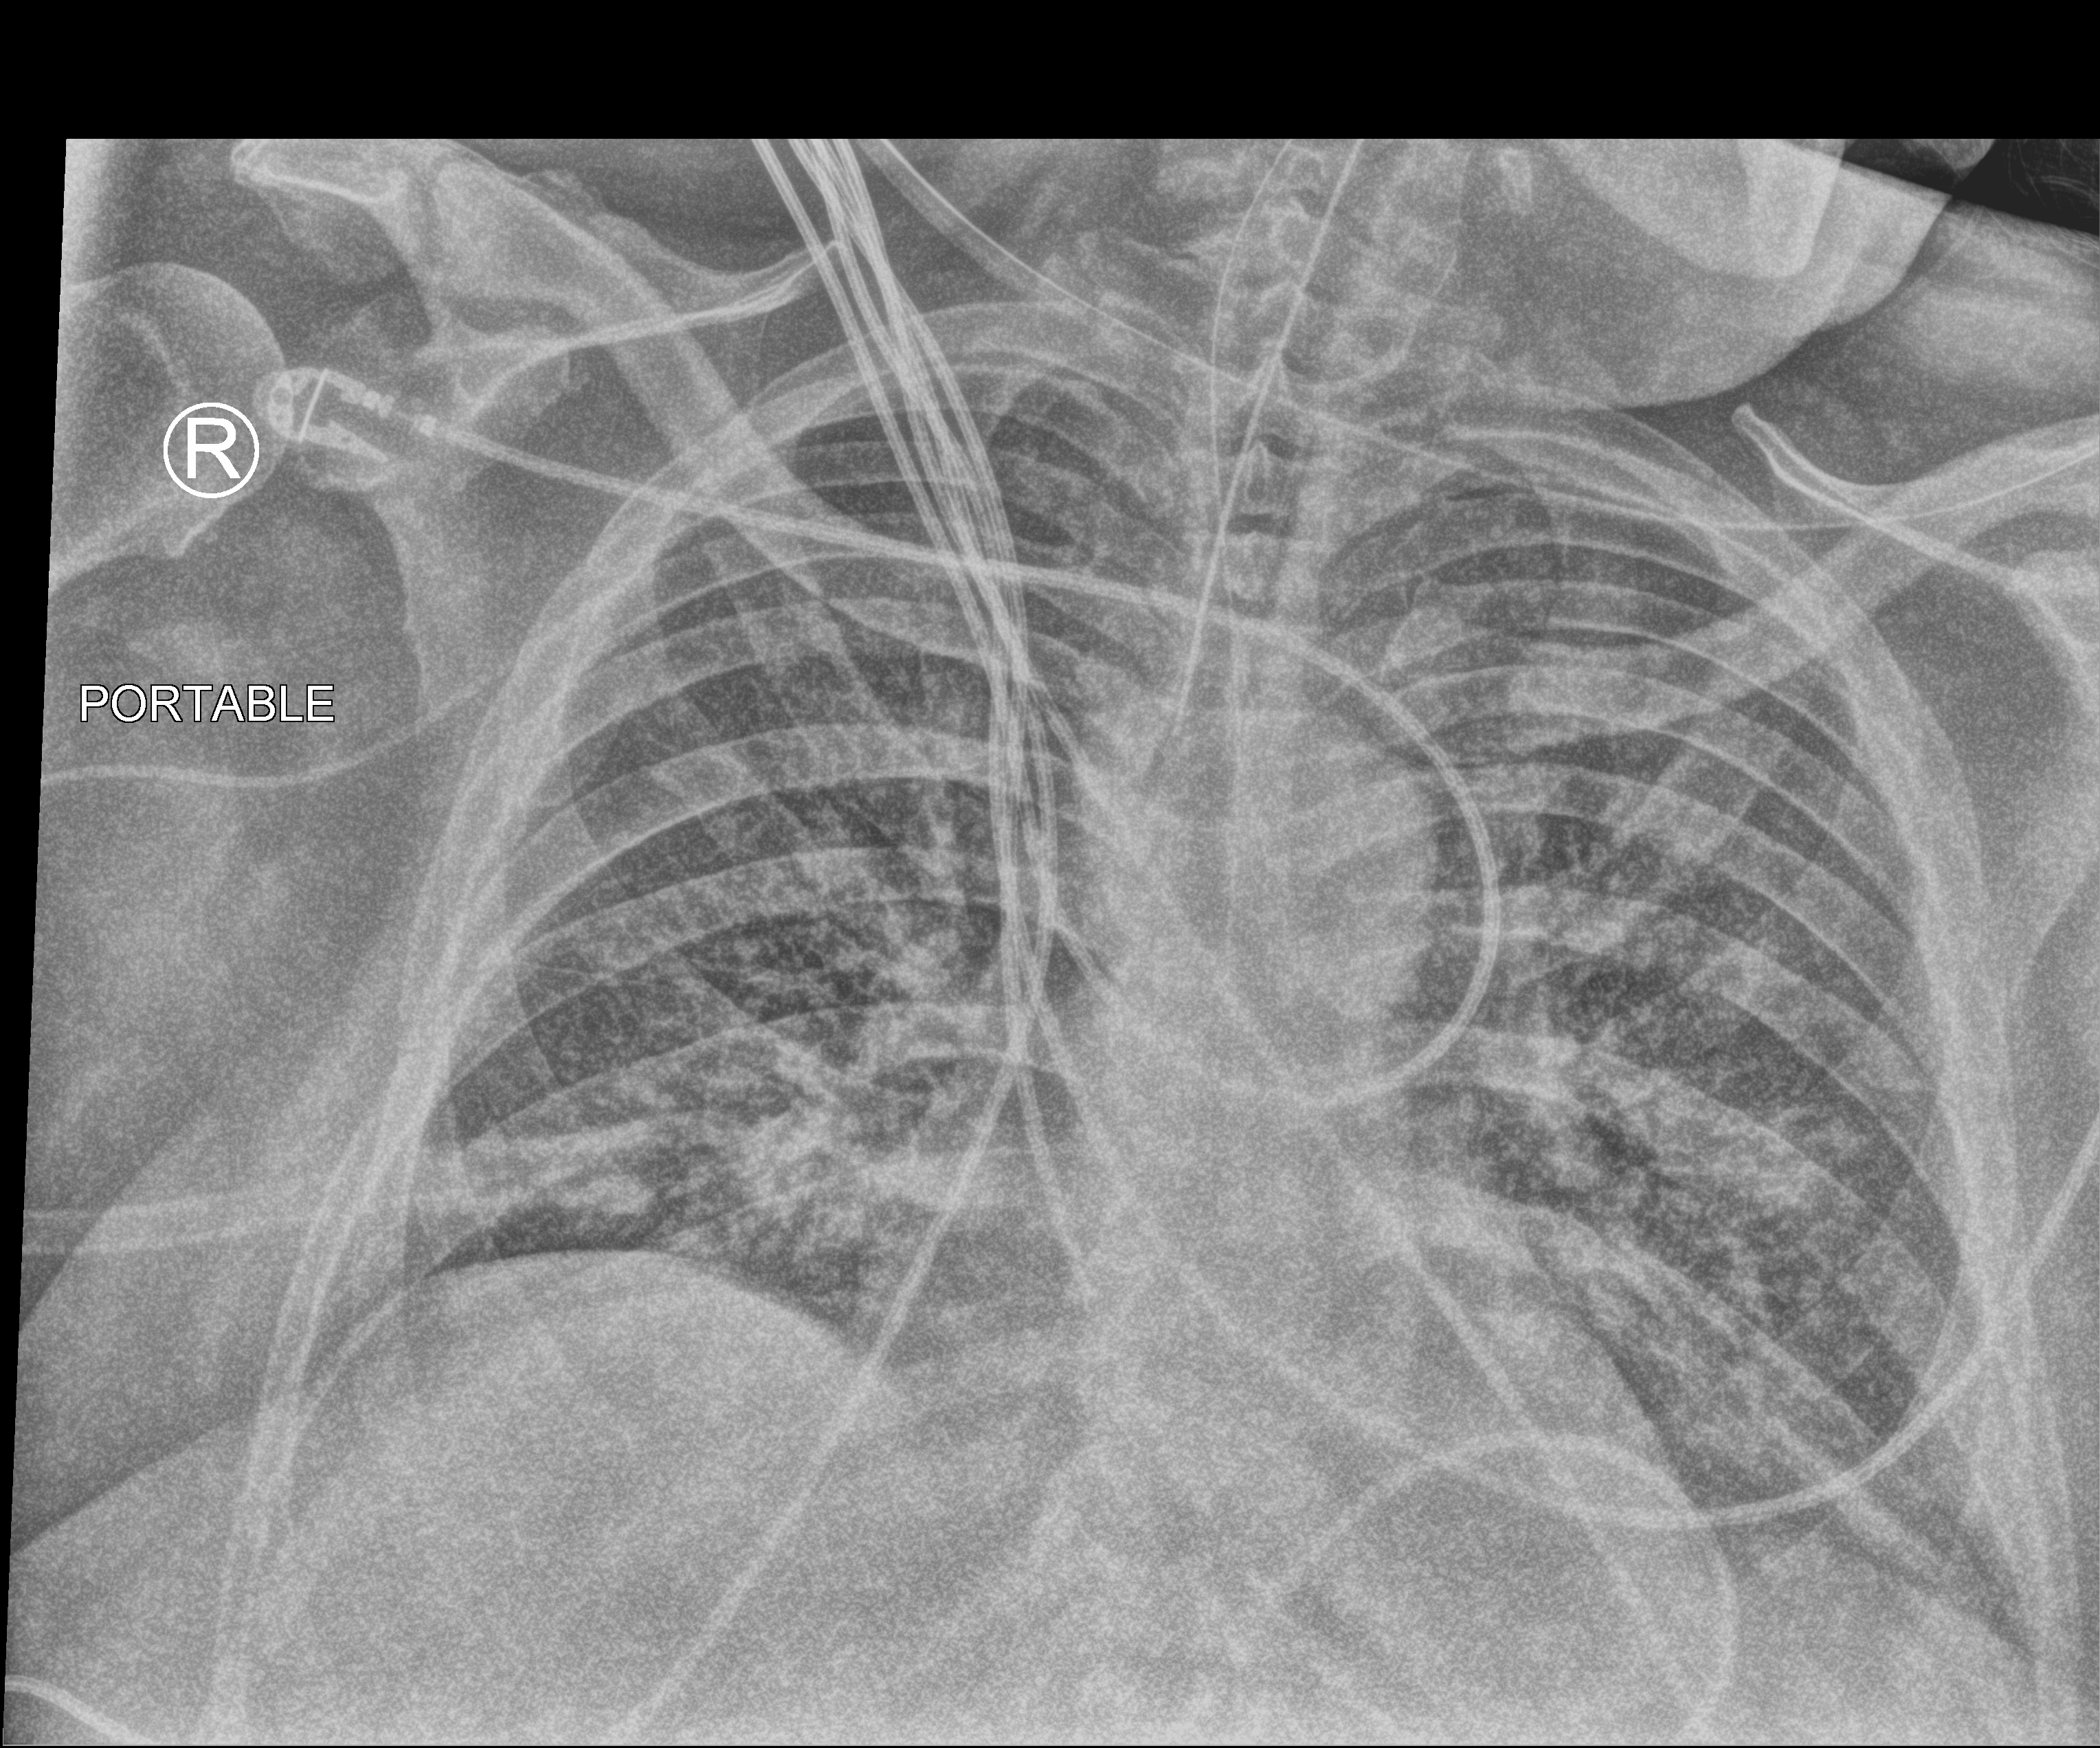
Bedside chest radiograph (computed radiography), anteroposterior (AP) projection. Patient hospitalised with COVID-19; male, aged 60–74 years.
Hospital-stay facts (about this admission, not read from this image; timing relative to this image not recorded): diabetes (admission record): yes.